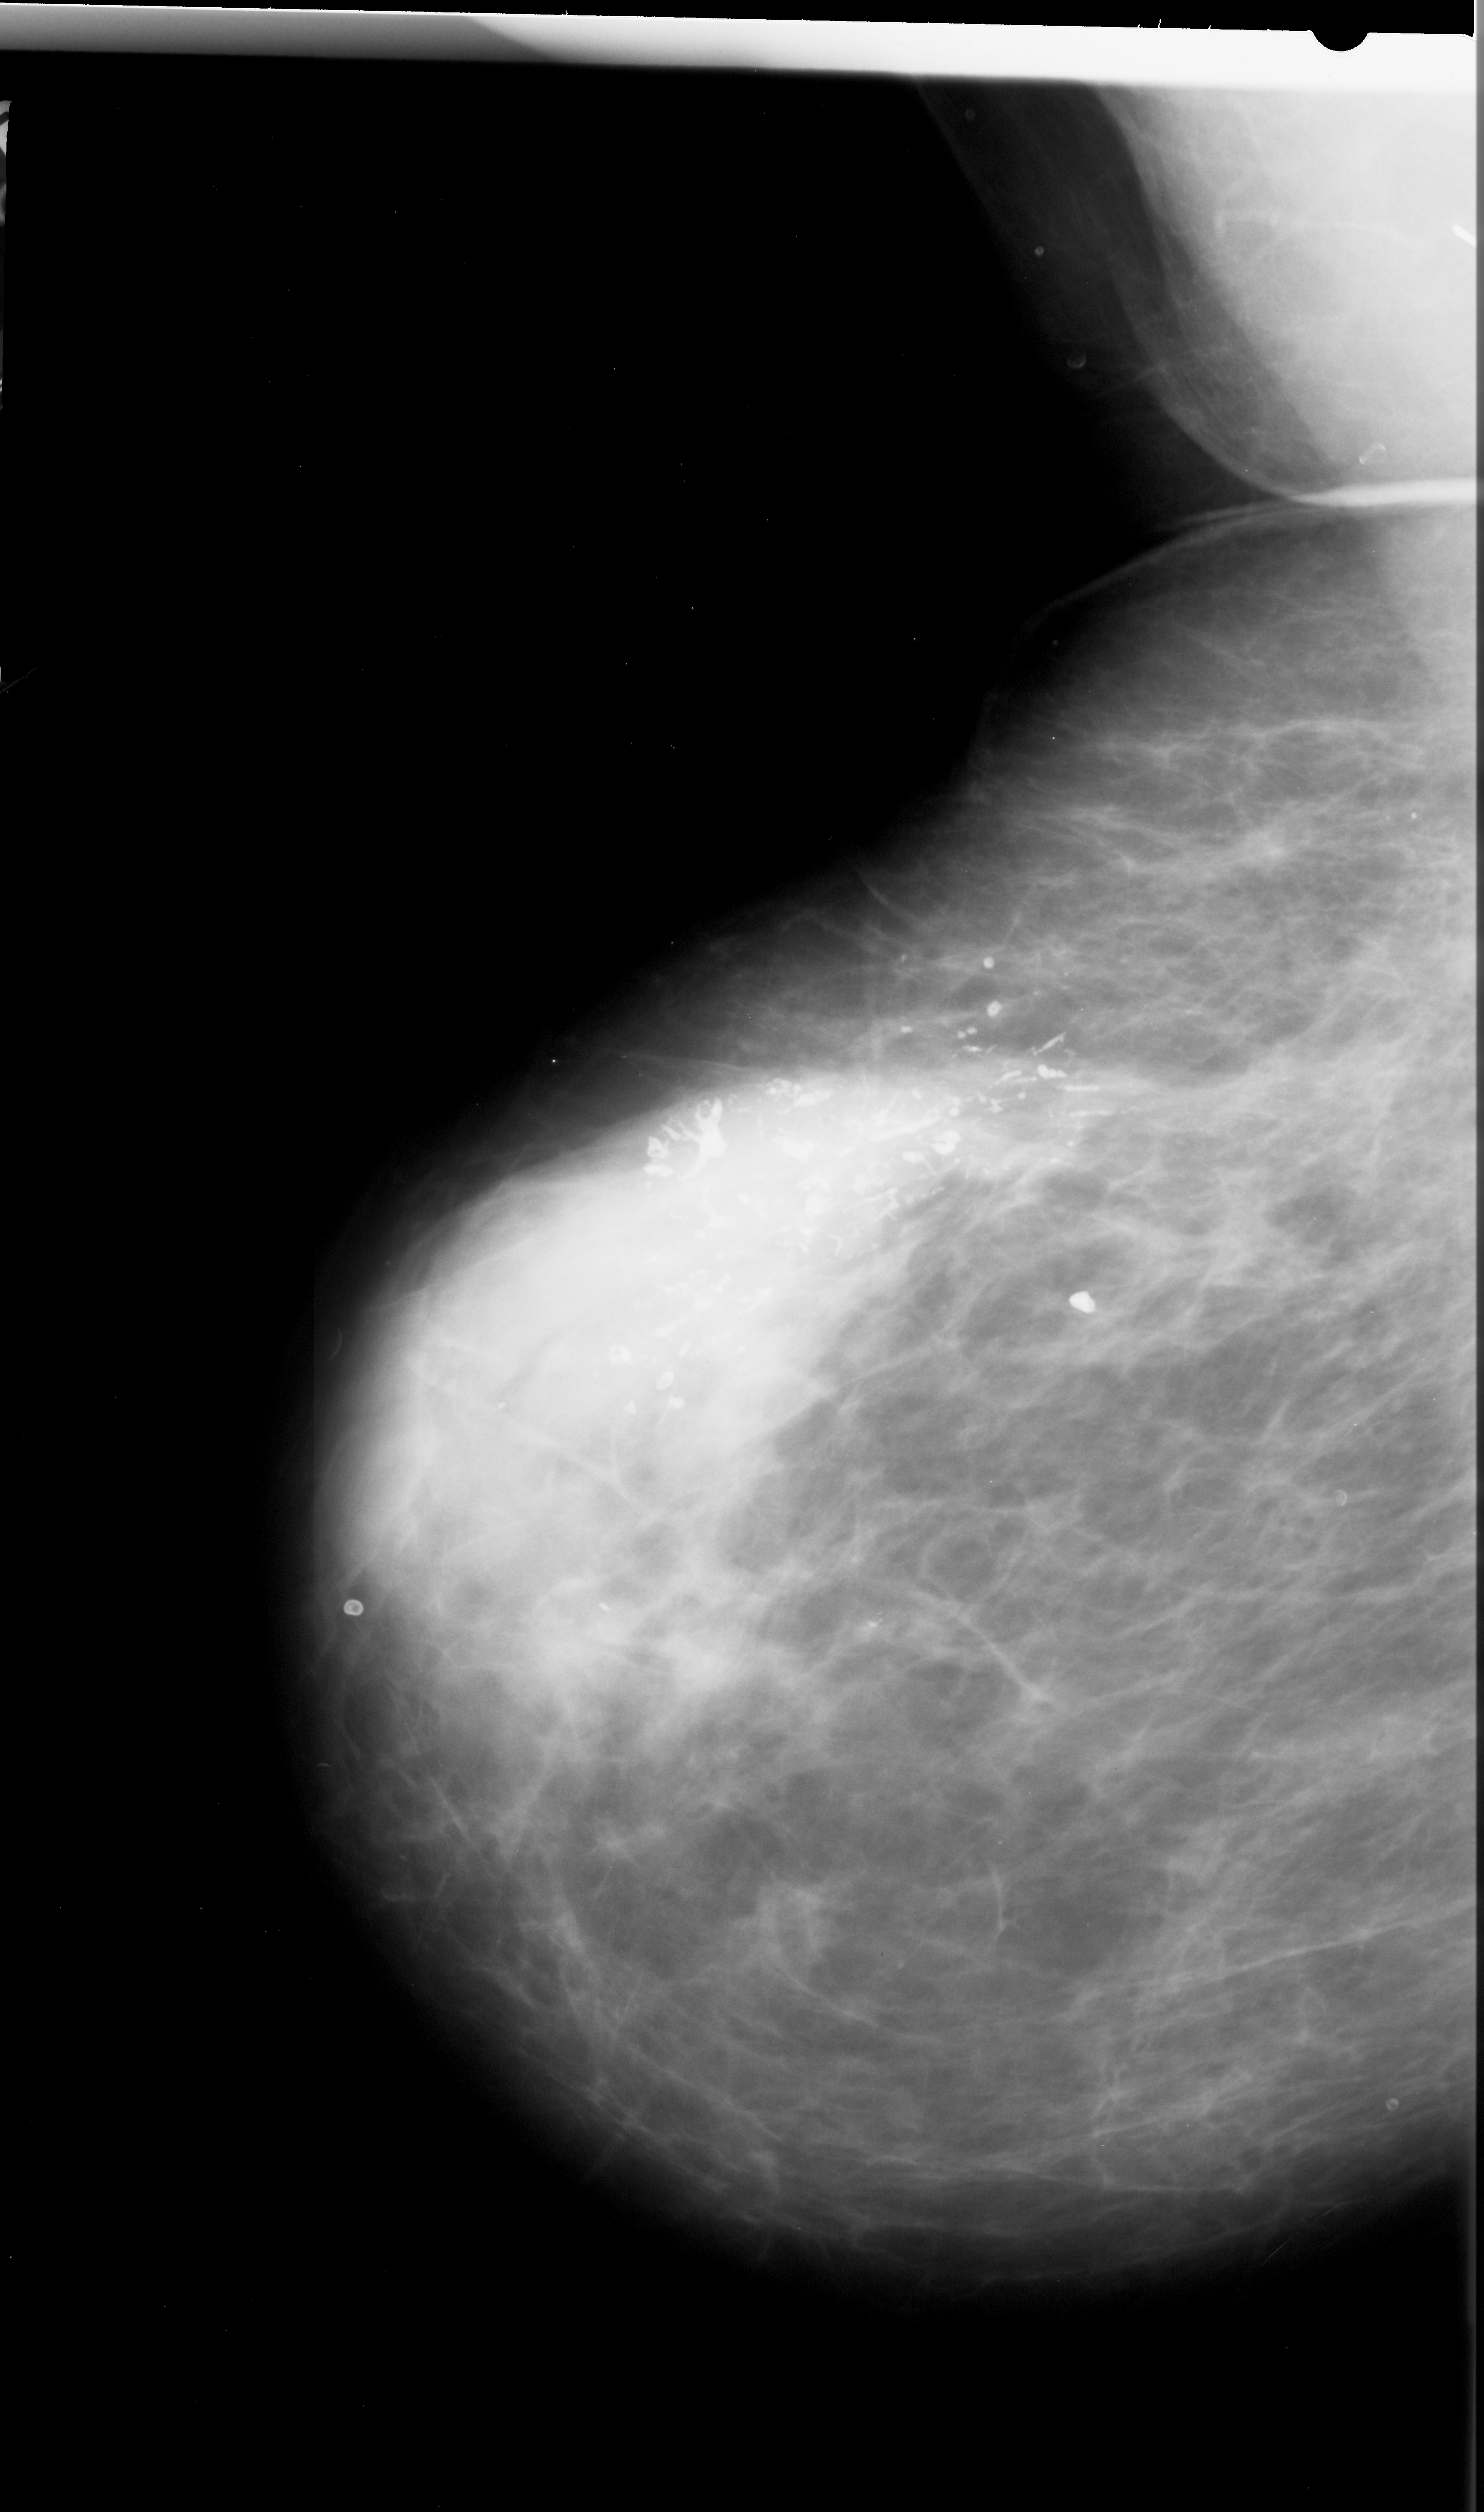
Digitized screen-film mammogram, left breast, MLO view, breast composition: extremely dense (BI-RADS density category 4 of 4).
Calcifications, morphology pleomorphic, distribution segmental; BI-RADS assessment category 5; subtlety rating 5 on a 1 (subtle) to 5 (obvious) scale; pathology (as recorded): malignant.